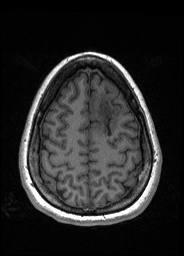
Pre-operative brain MRI before brain-tumour surgery, one axial slice. Slice 50 of 176 in the series (ordered by position). T1-weighted post-contrast. 1 mm slice thickness. 184 × 256 image matrix, field of view 180 × 250 mm. From the clinical record (not read from this slice): histopathology: Oligodendroglioma; WHO grade: 2; IDH mutation: yes.
Structures marked on this image (manually delineated by an expert):
- tumour: bounding box [x1, y1, x2, y2] px = [91, 97, 117, 135]